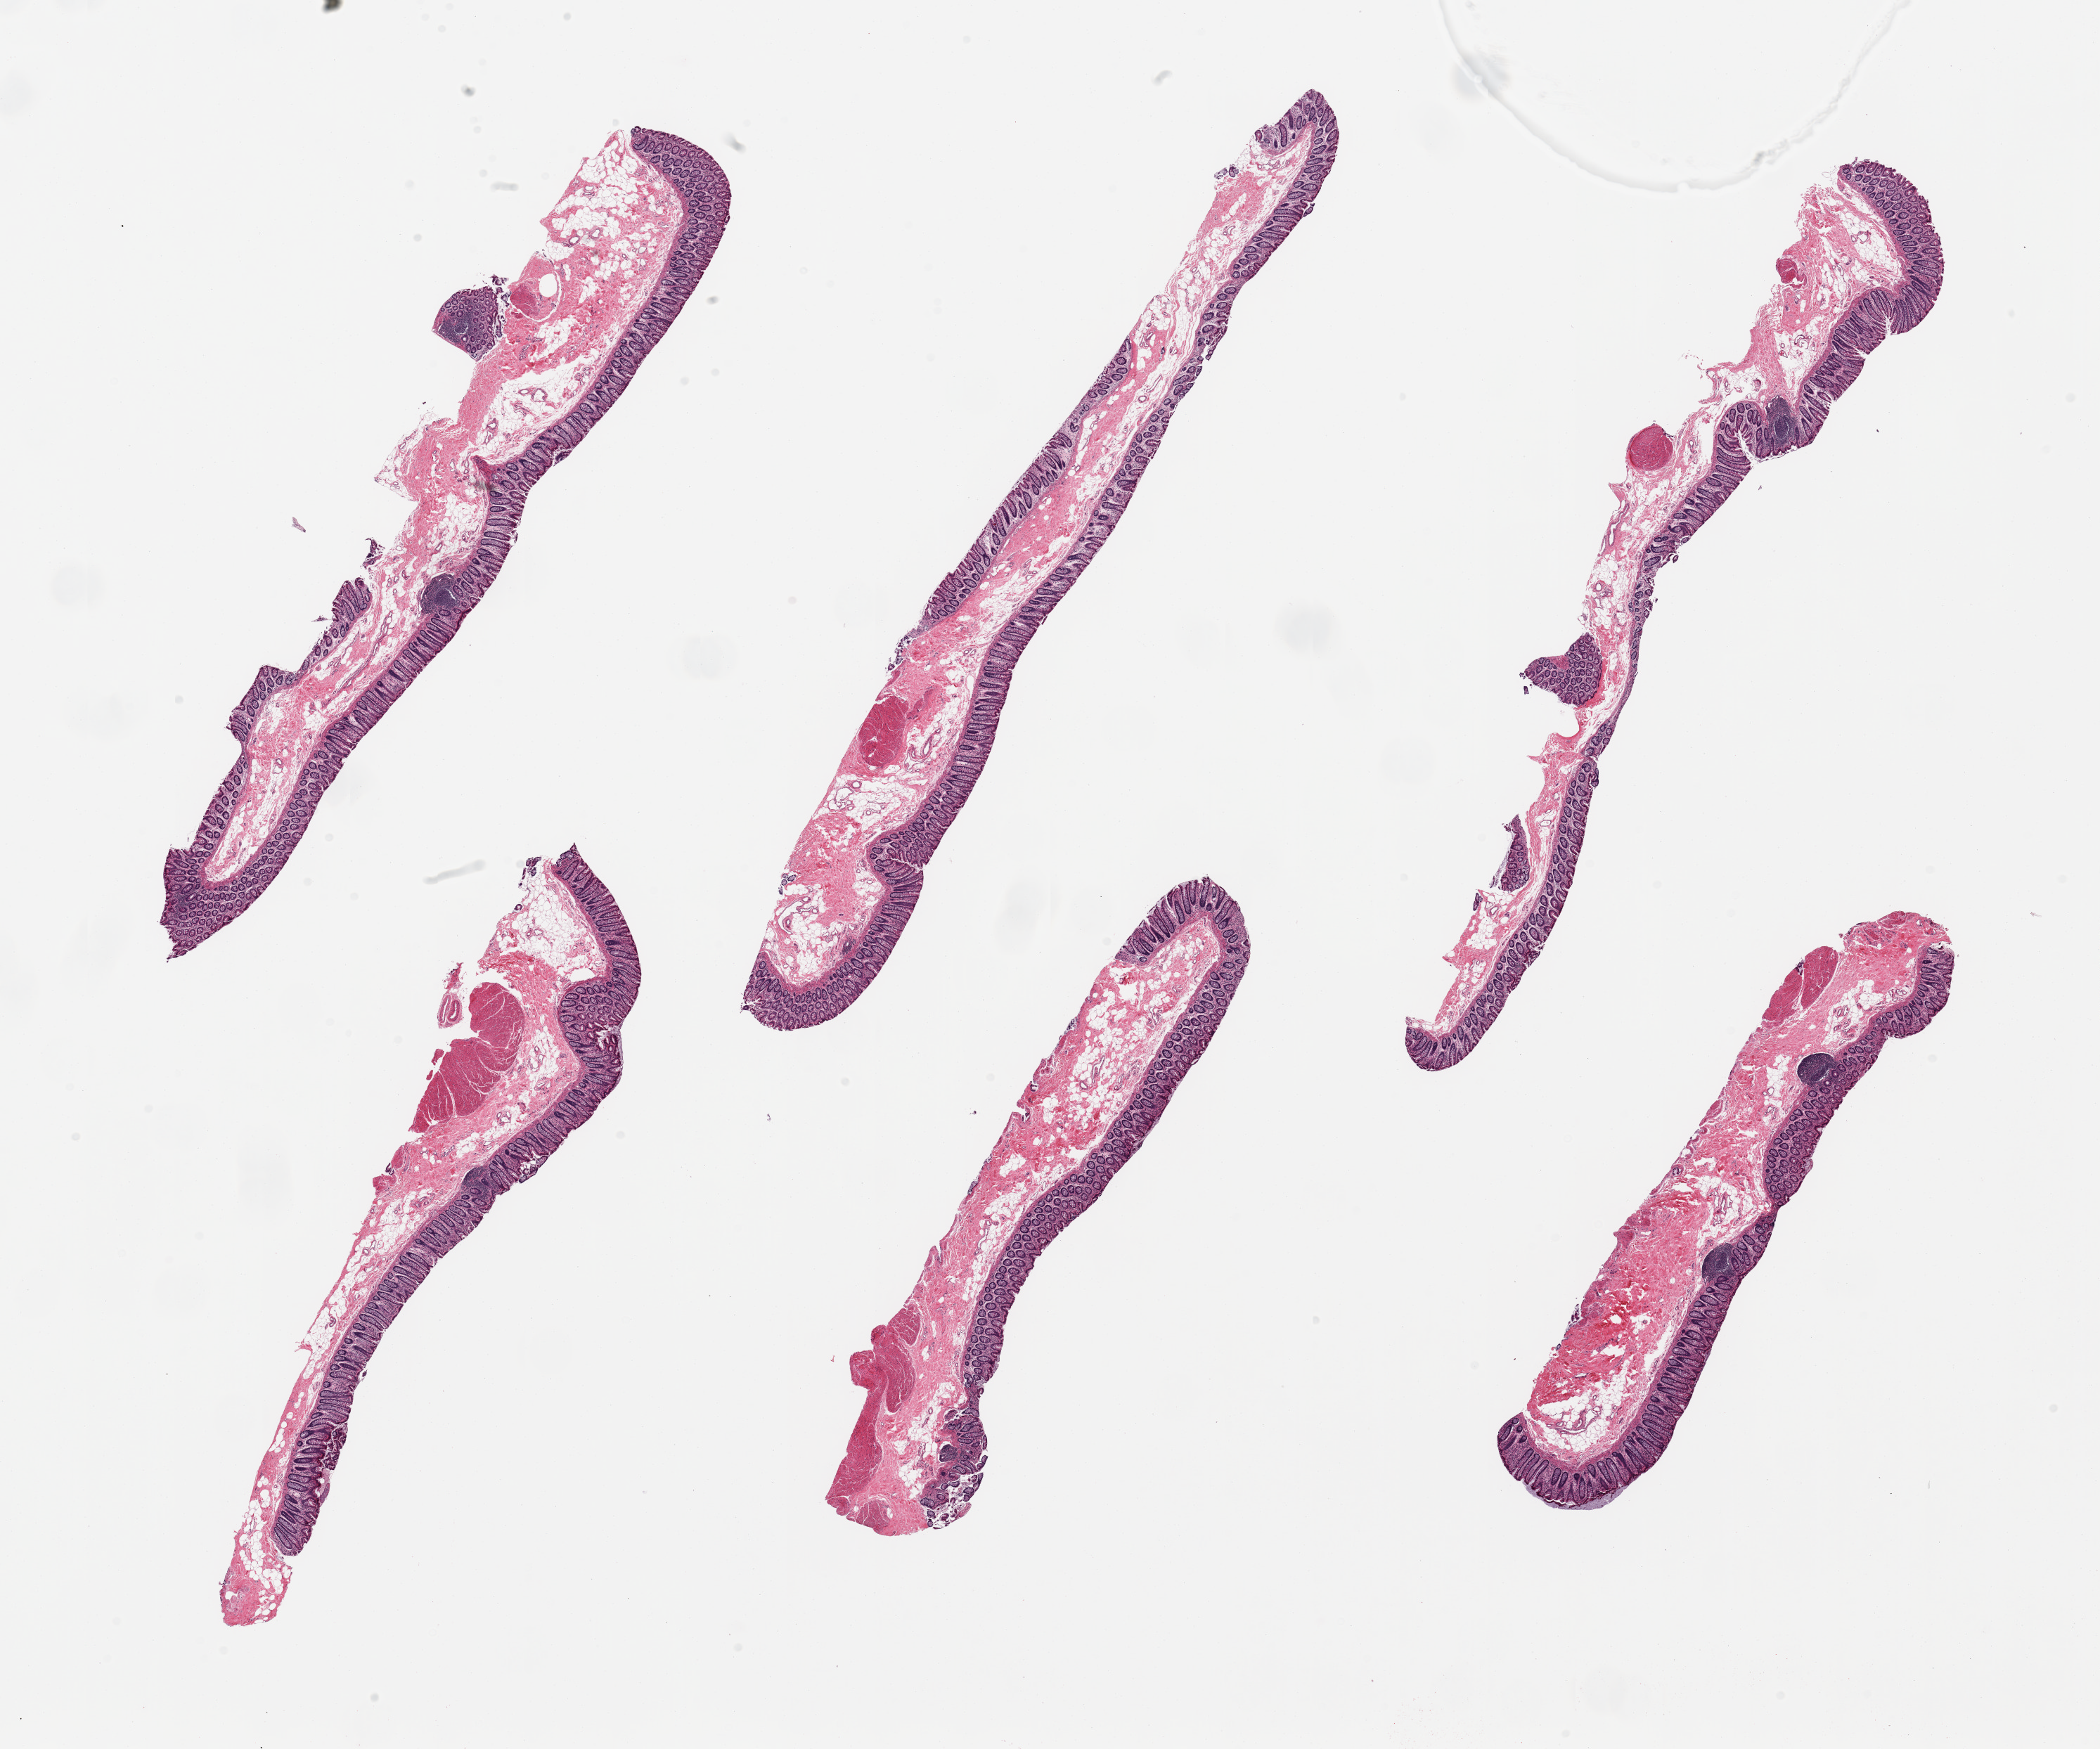
Digitized H&E-stained section — whole scanned area (about 23.6 x 19.7 mm, slide scanned at 20x) shown as a low-resolution overview. PAXgene-fixed, paraffin-embedded tissue. Sampled site (target tissue): transverse colon. Donor tissue sample. Female donor.
Review note (as recorded): 6 pieces, well preserved mucosa up to ~0.4mm, ~25% thickness.